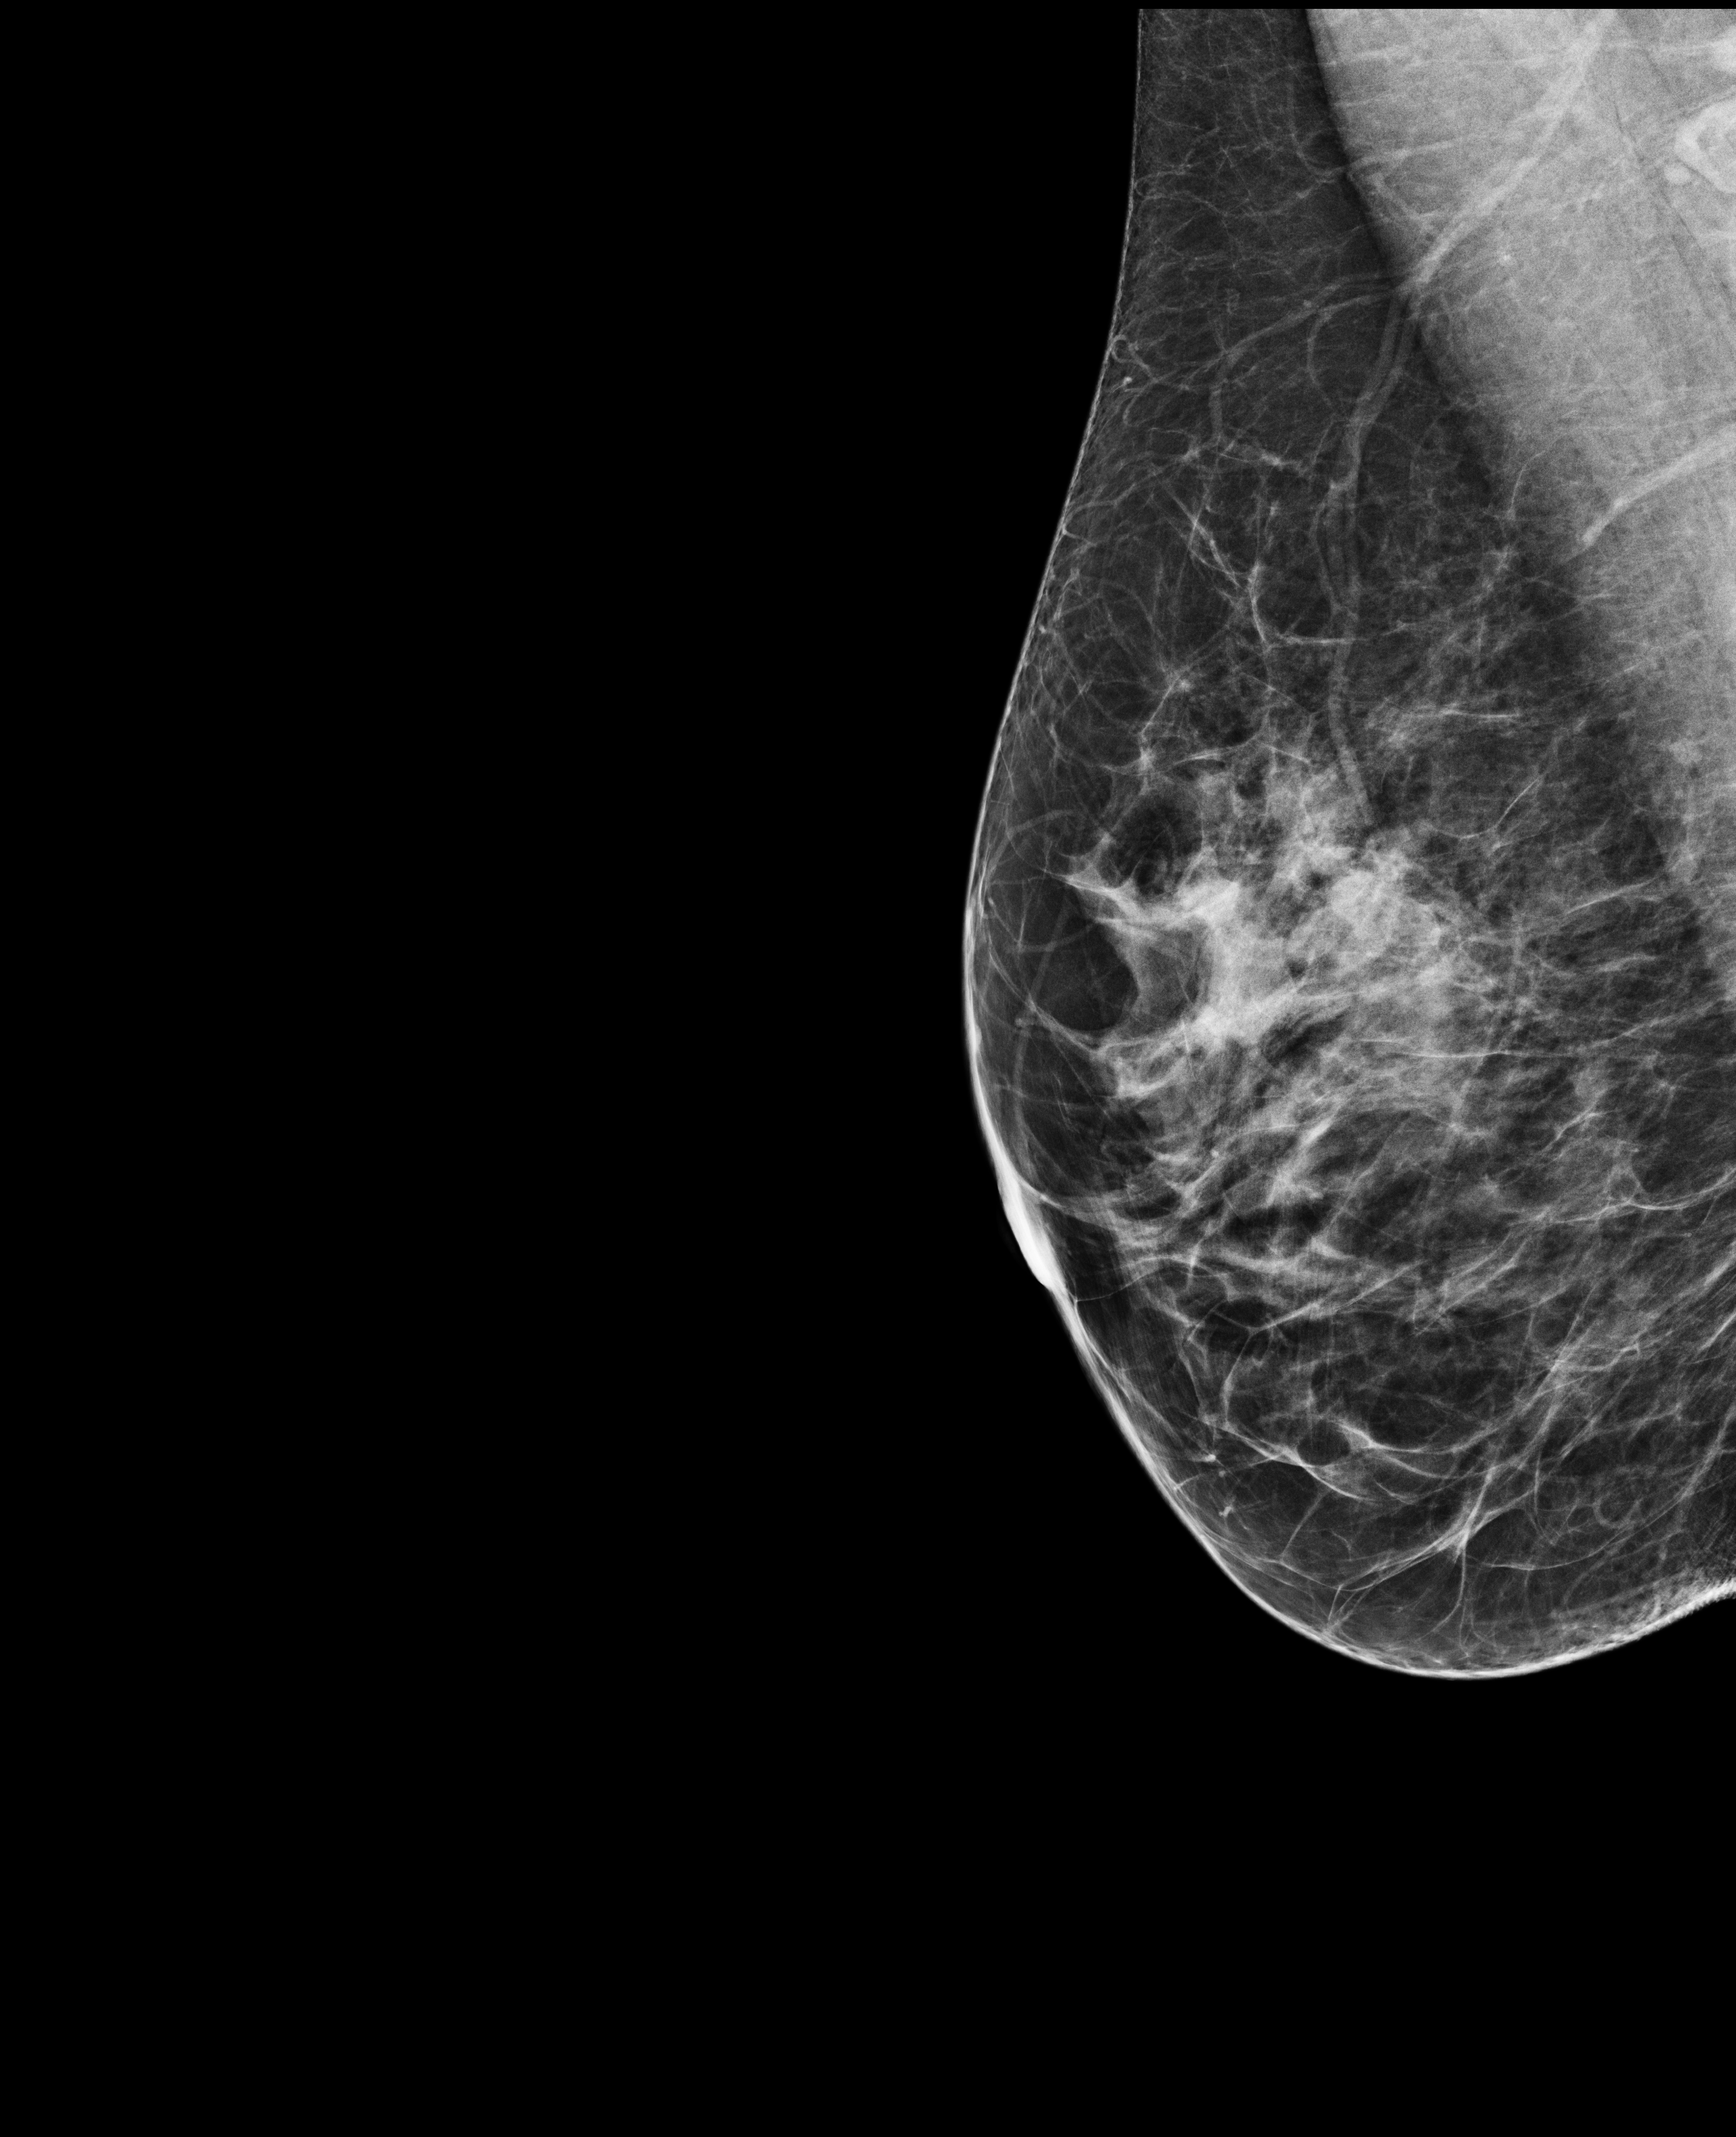
Annual screening mammography examination, compressed breast thickness 57 mm. Patient aged 43 years (female).
Image type: full-field digital mammogram. Breast: right. Projection: MLO view.